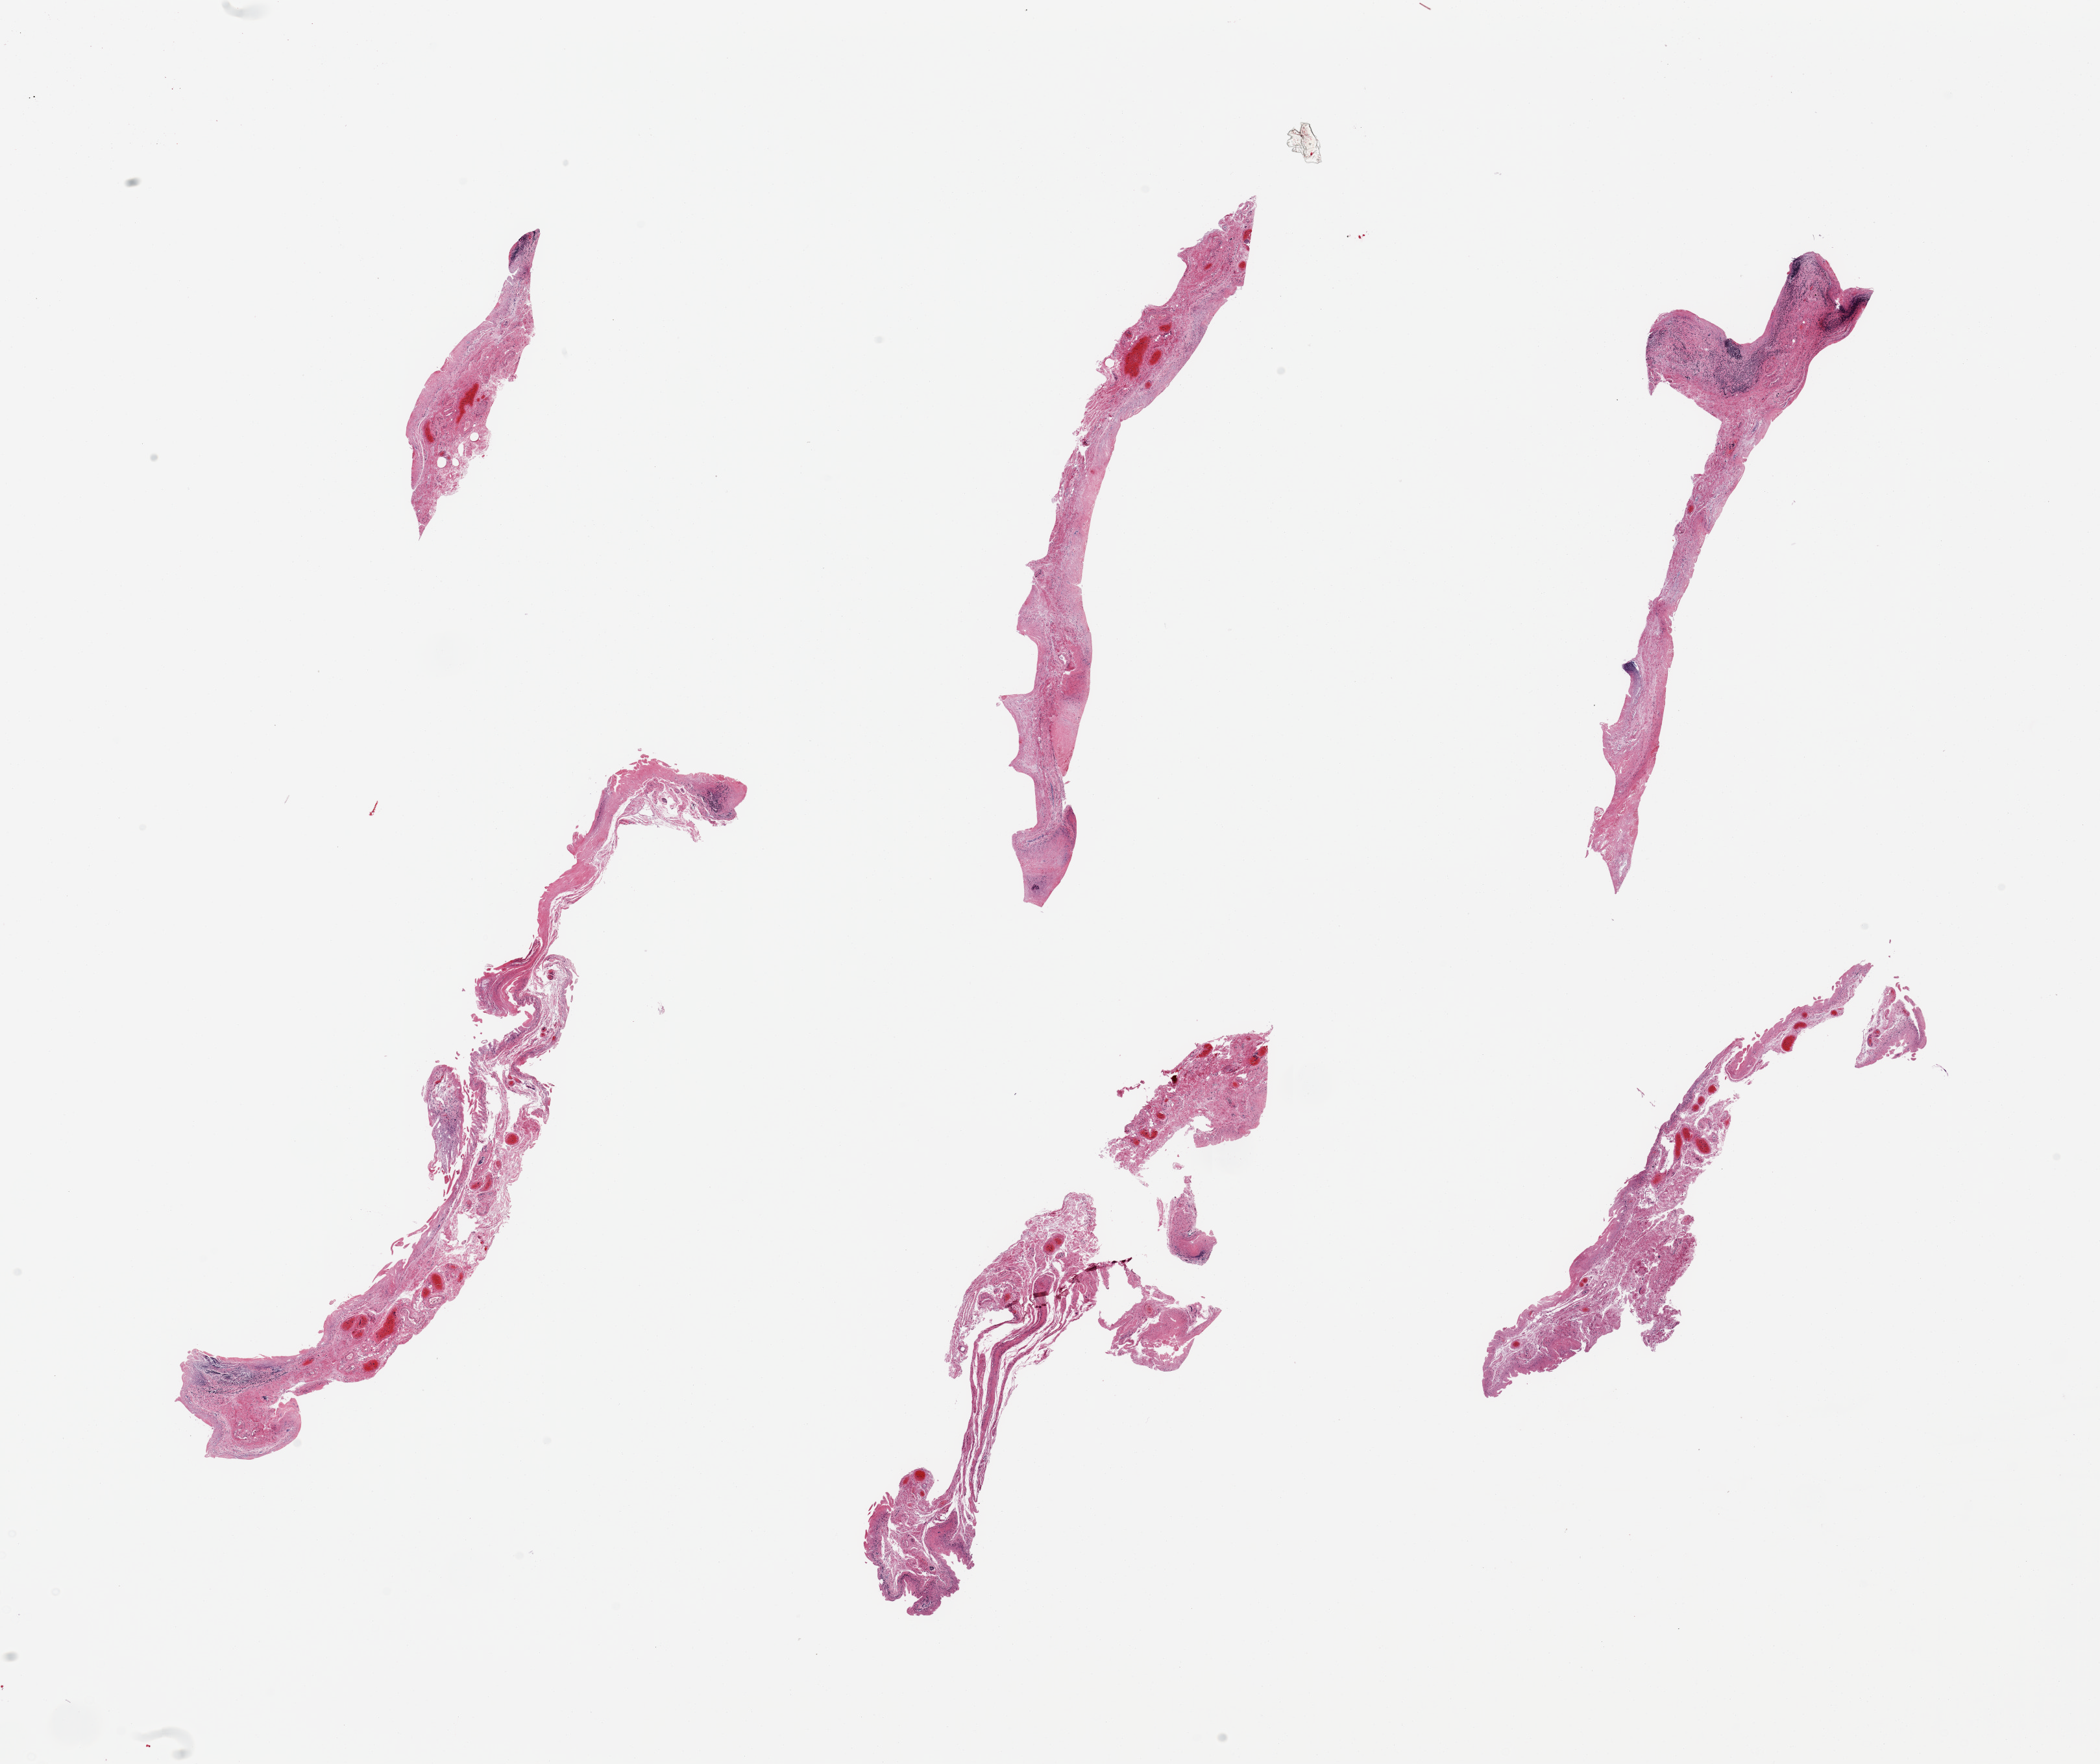
Hematoxylin and eosin (H&E) whole-slide image, low-resolution overview of the scanned area, about 25.6 x 21.5 mm; PAXgene-fixed, paraffin-embedded tissue; sampled site (target tissue): ileum; tissue donor sample.
Review note (as recorded): 6 pieces autolyzed mucosal stroma, trace lymphoid aggregates.